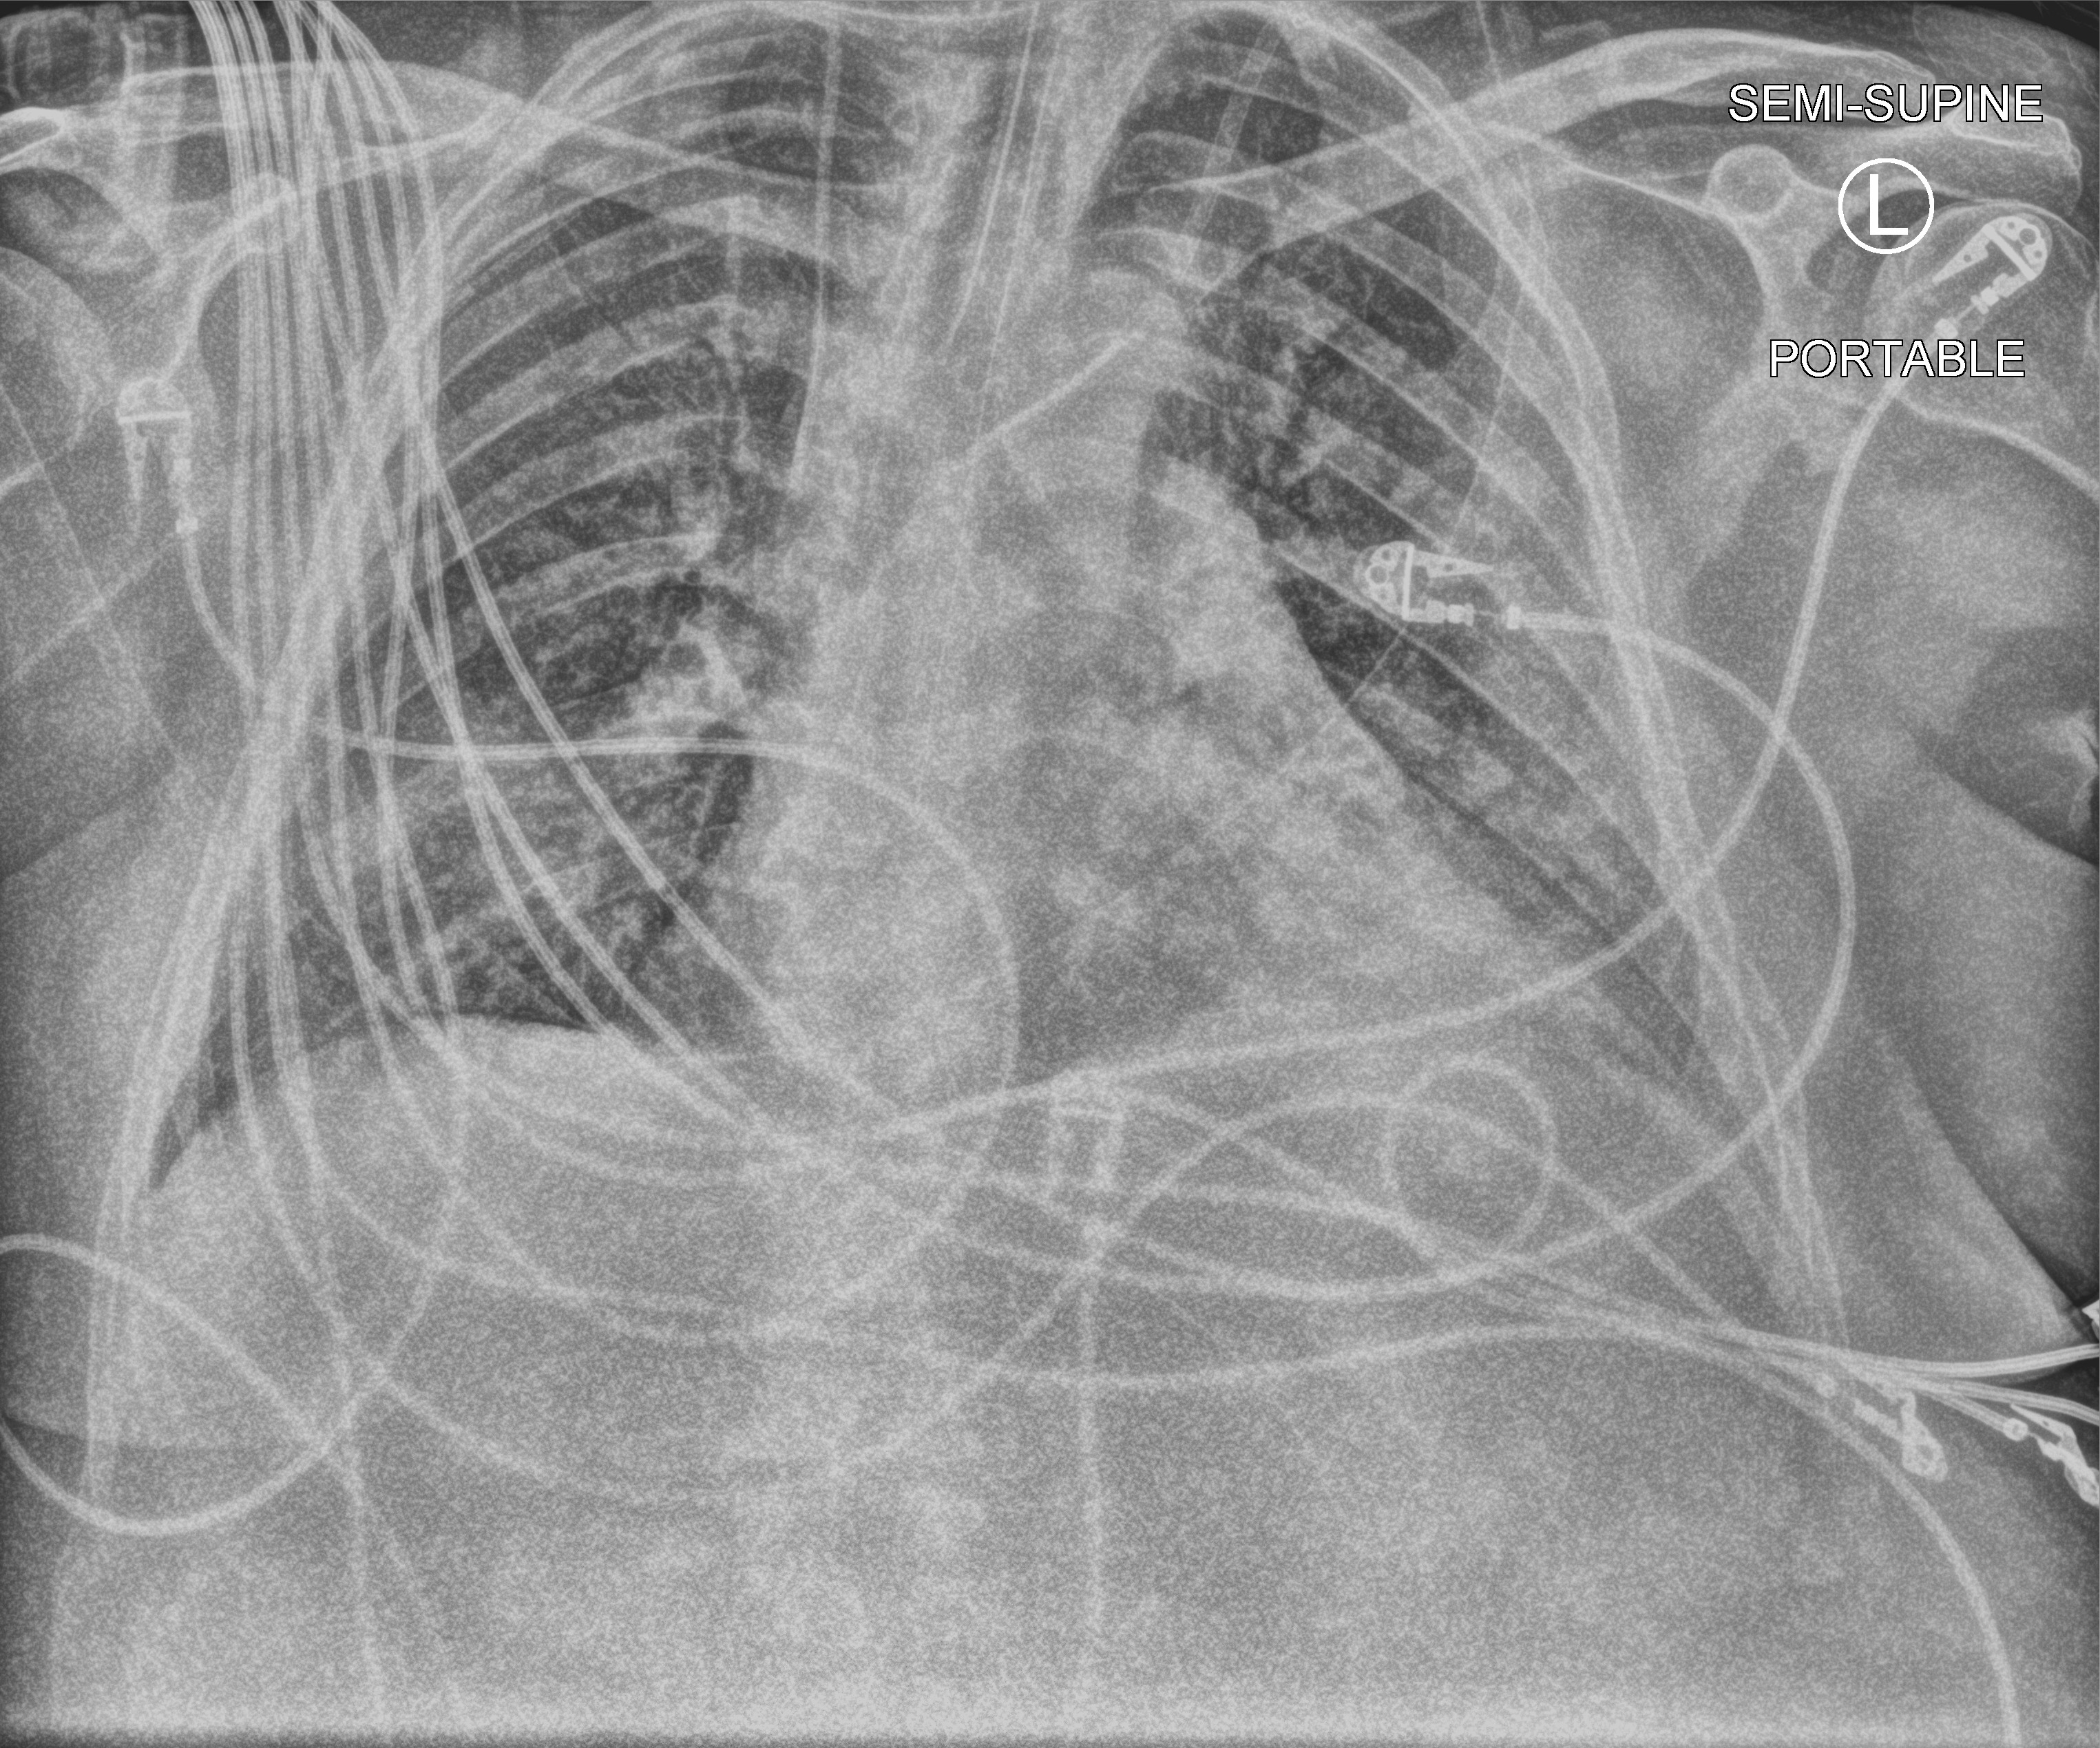
Portable chest radiograph, anteroposterior (AP) projection. Patient hospitalised with COVID-19; male, aged 18–59 years.
Hospital-stay facts (about this admission, not read from this image; timing relative to this image not recorded): mechanically ventilated during this hospital stay: yes.